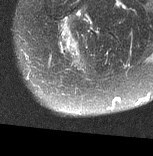
MRI of an extremity soft-tissue mass, one axial slice. Slice 17 of 77 in the series (ordered by position). T2-weighted fat-saturated. MR volume resampled by the dataset authors to the PET/CT grid (not the native acquisition matrix). 153 × 156 image matrix, field of view 149 × 152 mm. Female patient. From the clinical record (not read from this slice): histological type: synovial sarcoma; grade: intermediate; site of the primary tumour: right buttock.
Annotated regions visible in this slice (expert contour drawn on MRI and transferred to this co-registered scan by the dataset authors):
- gross tumour volume including surrounding oedema: bounding box (x1, y1, x2, y2) in pixels: (60, 20, 82, 67)